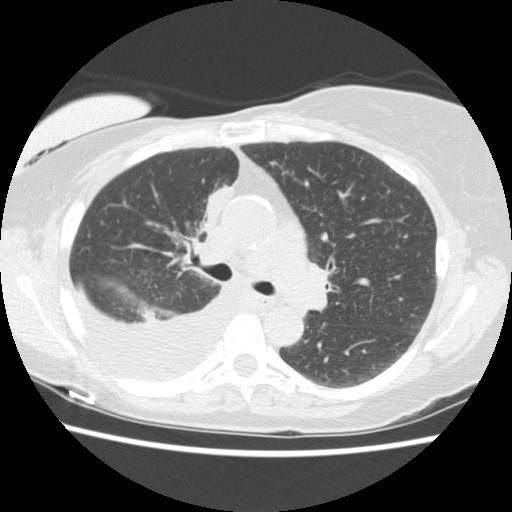
Low-dose screening chest CT, axial slice, third screening round (two years after baseline), lung window (W 1500 / L -600 HU), 2.5 mm slice thickness, 120 kVp, 512 × 512 image matrix. Female, age 56 years at enrolment.
- Lesion marked by an expert reader, bounding box [x1, y1, x2, y2] px = [183, 179, 245, 245].
- The screening reader recorded 2 non-calcified nodules or masses ≥4 mm on this exam; which of them this box marks is not recorded.
- Participant outcome: lung cancer diagnosed 160 days after this screen — adenocarcinoma, NOS, right upper lobe, stage IIIB (AJCC 6th edition), 8 mm at pathology.